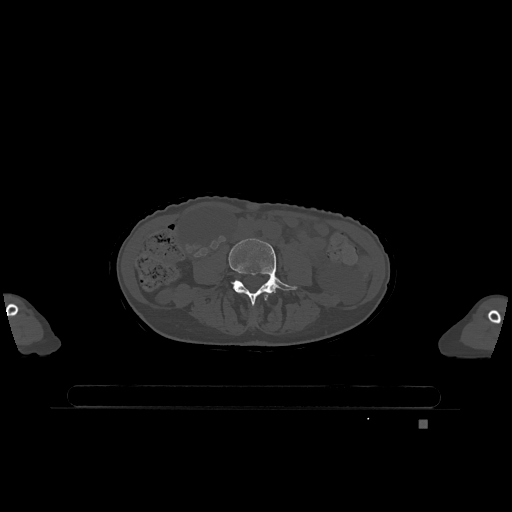
CT including the spine, one axial slice; slice 298 of 1317 in the series (ordered by position); bone window (W 1800 / L 400 HU); 0.5 mm slice thickness; 512 × 512 image matrix, field of view 500 × 500 mm. Patient: female, 74 years. Case-level facts recorded for this patient, not image findings: primary cancer: lung.
Outlined on this slice (semi-automatic segmentation, software-assisted and operator-edited):
- L3 vertebra: bounding box <264,293,270,301> (left, top, right, bottom; pixels)
- L4 vertebra: <229,239,297,305>